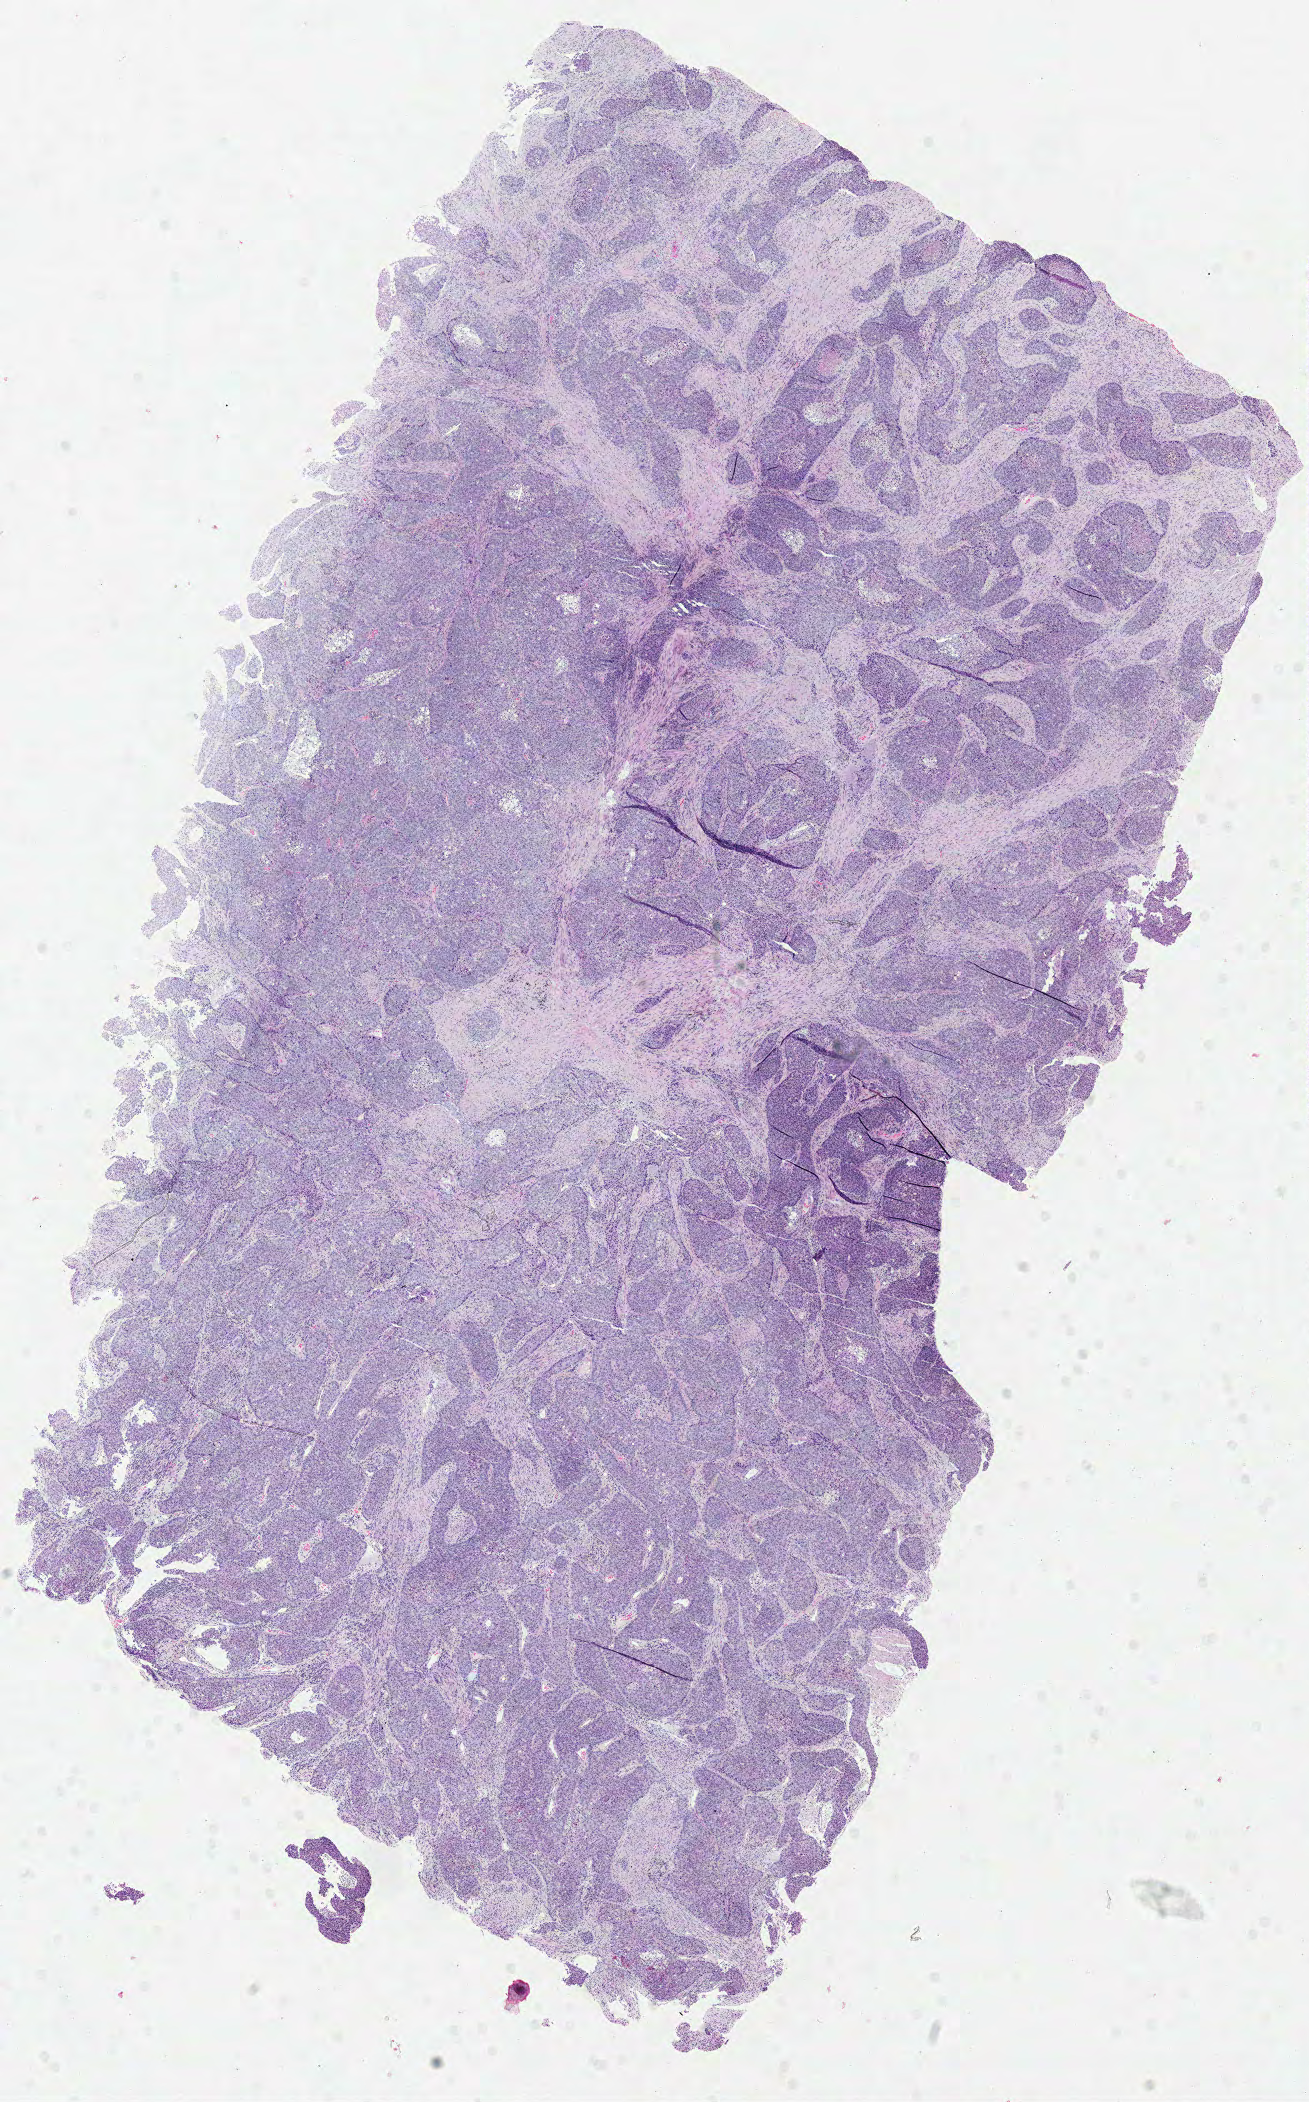
Whole-slide histology image, H&E-stained — shown as a low-resolution overview of the whole scanned area (about 10.3 x 16.6 mm, slide scanned at 40x); formalin-fixed paraffin-embedded (FFPE) diagnostic section; lung, primary tumour sample. Male, age 68 years at initial diagnosis.
- pathologic diagnosis: Squamous cell carcinoma, NOS (upper lobe, lung)
- TNM: T4 N0 M0
- AJCC pathologic stage: IIIB (6th edition)